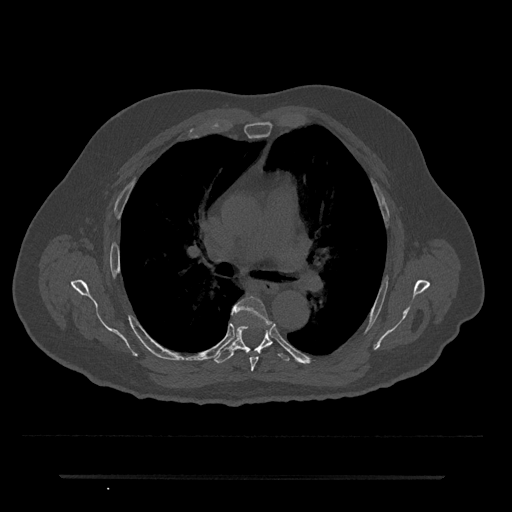
CT including the spine, one axial slice; slice 458 of 797 in the series (ordered by position); reconstruction kernel Br40s/3; 120 kVp; bone window (W 1800 / L 400 HU); 0.5 mm slice thickness; 512 × 512 image matrix, field of view 437 × 437 mm. Patient: male, 69 years. Case-level facts recorded for this patient, not image findings: primary cancer: prostate.
Annotated regions visible in this slice (semi-automatically segmented with operator editing):
- T5 vertebra: bounding box [x1, y1, x2, y2] px = [232, 296, 271, 371]
- T6 vertebra: [215, 319, 290, 364]